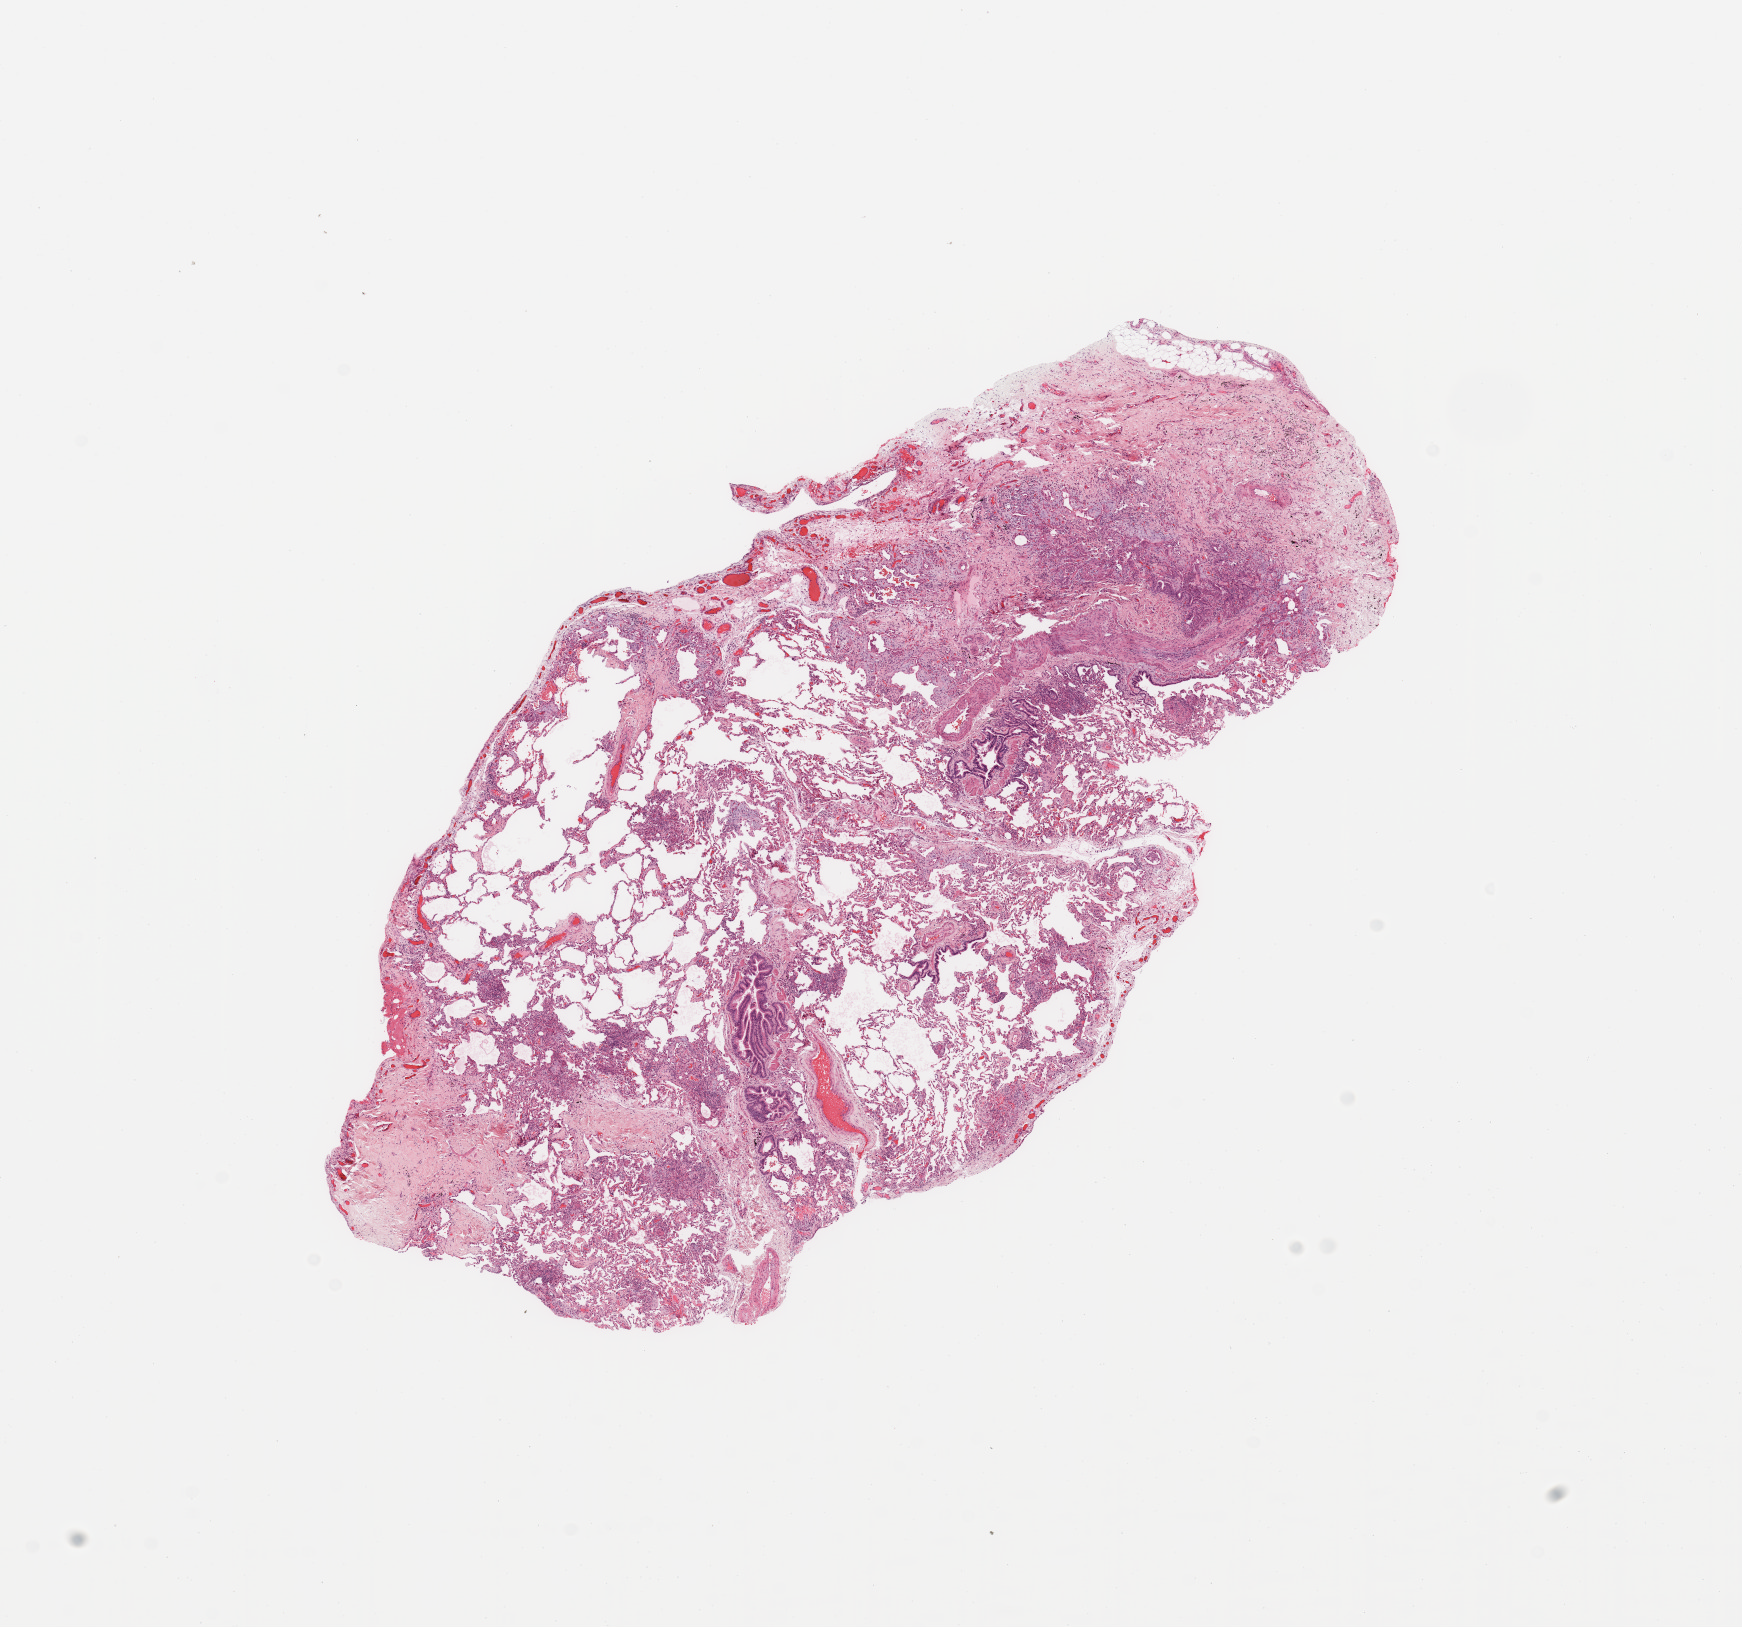
Hematoxylin and eosin (H&E) stained whole-slide image, whole scanned area (about 13.8 x 12.9 mm) shown as a low-resolution overview; normal (non-tumour) tissue sample, lung. 70-year-old male patient.
* this section: normal (non-tumour) tissue from the same patient
* patient diagnosis: Squamous cell carcinoma, NOS